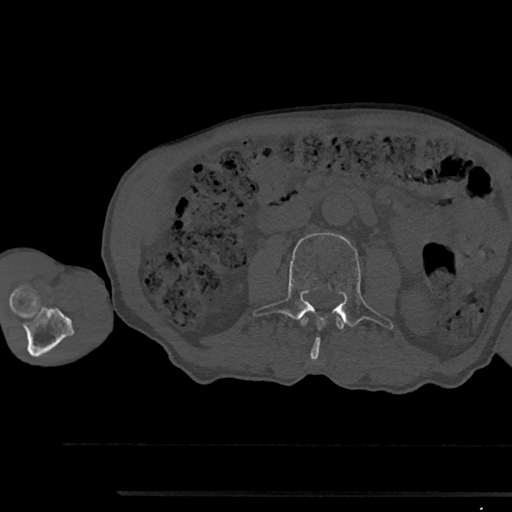
CT including the spine, one axial slice; position 501 of 797 along the scan axis; reconstruction kernel Br40s/3; bone window (W 1800 / L 400 HU); 0.5 mm slice thickness; 512 × 512 image matrix, field of view 367 × 367 mm. Patient: male, 79 years. From the clinical record (not read from this slice): primary cancer: prostate.
Structures marked on this image (semi-automatic segmentation, software-assisted and operator-edited):
- L2 vertebra: bounding box [x1, y1, x2, y2] px = [301, 317, 344, 330]
- L3 vertebra: [253, 233, 393, 360]